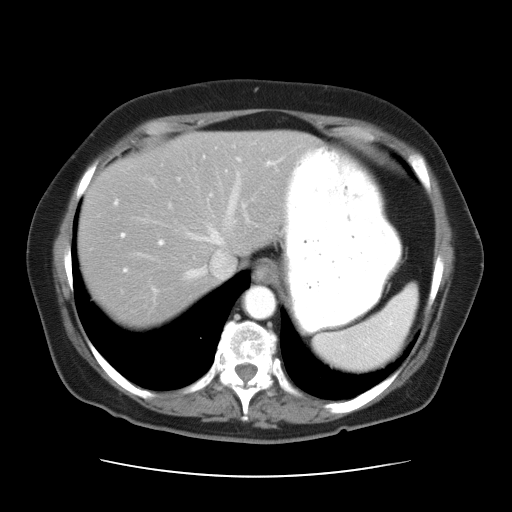
Contrast-enhanced abdominal CT, one axial slice. Position 27 of 34 along the scan axis. Reconstruction kernel STANDARD. 120 kVp. Intravenous contrast given. Soft-tissue window (W 400 / L 40 HU). 7.5 mm slice thickness. 512 × 512 image matrix, field of view 360 × 360 mm. Female patient, age 65 years. Case-level facts recorded for this patient, not image findings: diagnosis: colorectal cancer liver metastases, imaged before liver resection; multiple liver metastases: yes; largest metastasis: 2.2 cm.
Structures marked on this image (manually delineated by an expert):
- hepatic veins: bounding box <113,171,242,280> (left, top, right, bottom; pixels)
- liver: <80,133,308,321>
- planned liver remnant (the part of the liver to remain after resection): <80,133,307,322>
- portal vein (with intrahepatic branches): <121,155,248,237>